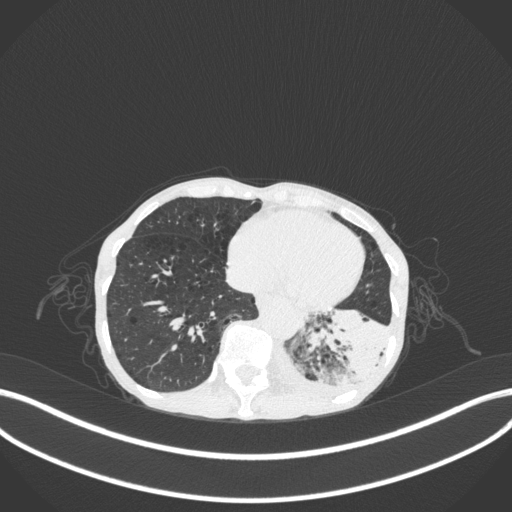
Chest CT, one axial slice. Position 59 of 347 along the scan axis. Lung window (W 1500 / L -600 HU). 512 × 512 image matrix, field of view 400 × 400 mm. Patient: female, 70 years. Case-level facts recorded for this patient, not image findings: clinical TNM (as recorded): T3 N0 M0; histopathological grade: G3.
Outlined on this slice (bounding box drawn by a radiologist):
- lung tumour (recorded histology: small cell carcinoma): box from (x=296, y=301) to (x=395, y=392) px